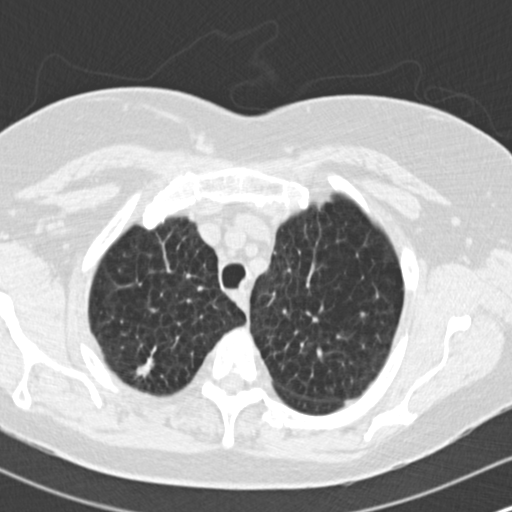
Axial slice from a low-dose chest CT screening exam; baseline screening round; lung window (W 1500 / L -600 HU); 2 mm slice thickness; slice 29 of 172 in the series; 512 × 512 image matrix, field of view 310 × 310 mm. Female participant, aged 73 years at enrolment.
- Lesion marked by an expert reader, box from (x=120, y=340) to (x=173, y=388) px.
- The screening reader recorded 2 non-calcified nodules or masses ≥4 mm on this exam (right upper lobe, right upper lobe); which of them this box marks is not recorded.
- Official screen result: positive, change unspecified: nodule(s) >= 4 mm or enlarging nodule(s), mass(es), or other non-specific abnormalities suspicious for lung cancer.
- Later outcome: lung cancer diagnosed 601 days after this screen — adenocarcinoma, NOS, right upper lobe, moderately differentiated (G2), stage IB (AJCC 6th edition), 15 mm at pathology.